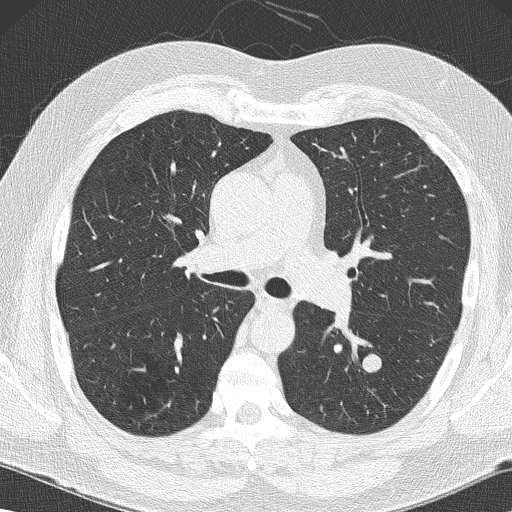
Axial slice from a low-dose chest CT screening exam; baseline annual screen; lung window (W 1500 / L -600 HU); 2 mm slice thickness. Male, age 59 years at enrolment. Former smoker at enrolment.
- Expert-annotated lung lesion, bounding box [x1, y1, x2, y2] px = [346, 347, 389, 383].
- The screening reader recorded 2 non-calcified nodules or masses ≥4 mm on this exam (left lower lobe, left lower lobe); which of them this box marks is not recorded.
- Official screen result: positive, change unspecified: nodule(s) >= 4 mm or enlarging nodule(s), mass(es), or other non-specific abnormalities suspicious for lung cancer.
- Participant outcome: lung cancer diagnosed 61 days after this screen — large cell carcinoma, NOS, left lower lobe, poorly differentiated (G3), stage IA (AJCC 6th edition), 14 mm at pathology.